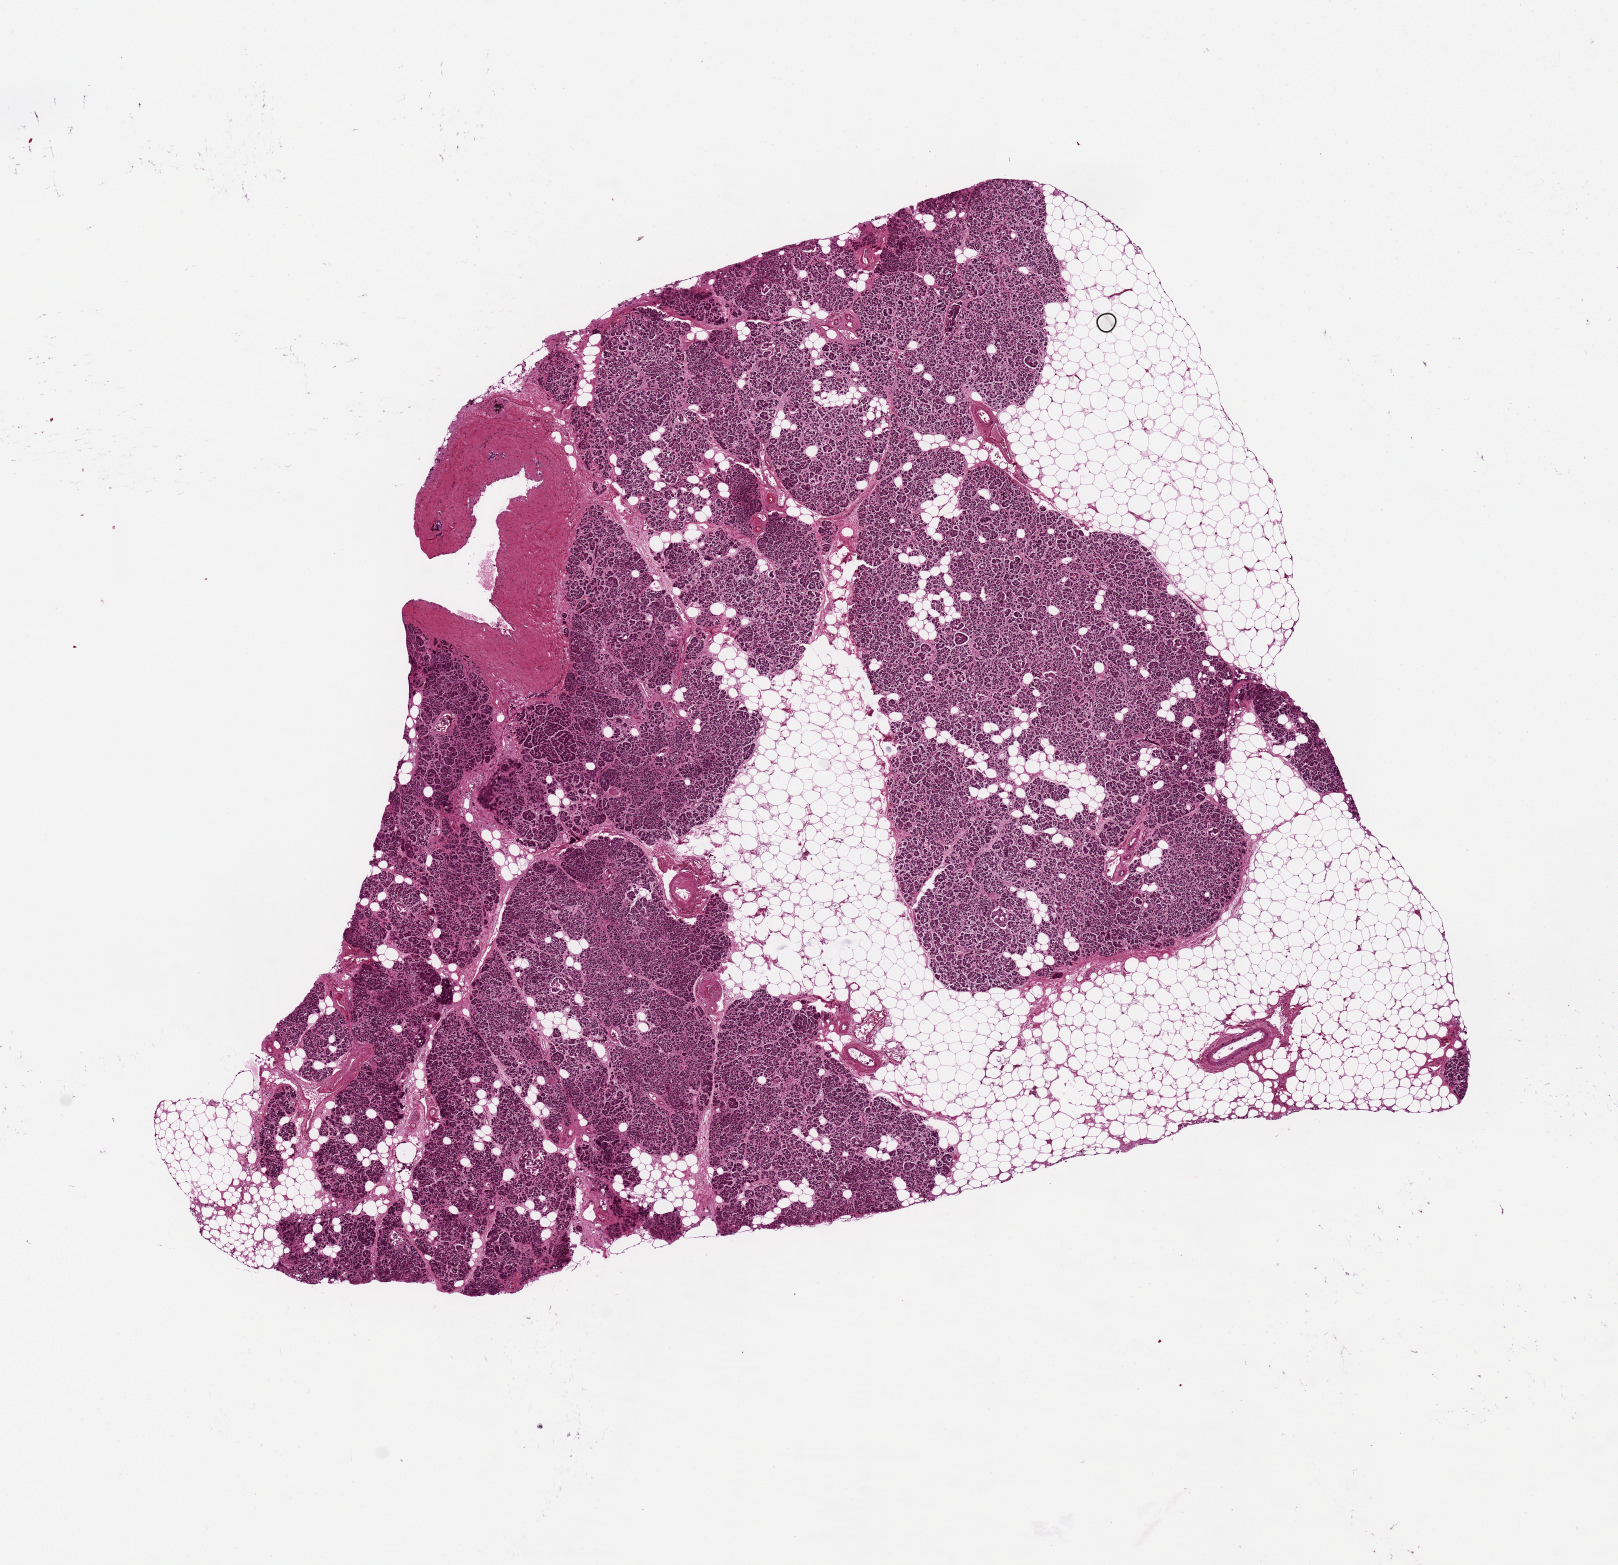
Hematoxylin and eosin (H&E) whole-slide image — shown as a low-resolution overview of the whole scanned area (about 12.8 x 12.4 mm). PAXgene-fixed, paraffin-embedded tissue. Section of pancreas (target tissue). Donor tissue sample. Donor: male.
* pathologist's review note for this sample: Aliquot contains about 40% fat